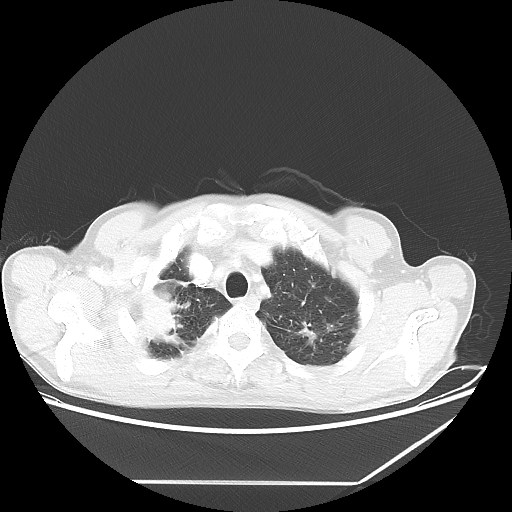
Chest CT, one axial slice. Slice 56 of 65 in the series (ordered by position). Lung window (W 1500 / L -600 HU). 5 mm slice thickness. 512 × 512 image matrix. Patient: male, 68 years. From the clinical record (not read from this slice): clinical TNM (as recorded): T3 N3 M0.
Outlined on this slice (bounding box drawn by a radiologist):
- lung tumour (recorded histology: adenocarcinoma): bounding box [x1, y1, x2, y2] px = [123, 282, 189, 354]